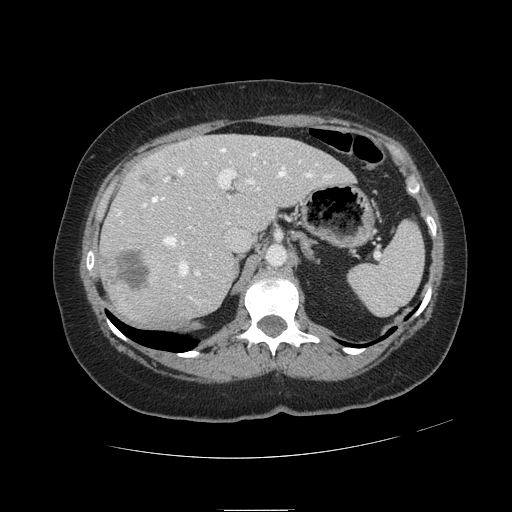
Contrast-enhanced abdominal CT, one axial slice. Position 73 of 121 along the scan axis. Intravenous contrast given. Soft-tissue window (W 400 / L 40 HU). 2.5 mm slice thickness. 512 × 512 image matrix, field of view 400 × 400 mm. Female patient, age 52 years. Case-level facts recorded for this patient, not image findings: diagnosis: colorectal cancer liver metastases, imaged before liver resection; multiple liver metastases: yes; largest metastasis: 6.3 cm; disease in both lobes: no.
Outlined on this slice (manually delineated by an expert):
- hepatic veins: box from (x=118, y=149) to (x=331, y=299) px
- liver: (x=101, y=135)–(x=353, y=323)
- planned liver remnant (the part of the liver to remain after resection): (x=167, y=135)–(x=352, y=230)
- portal vein (with intrahepatic branches): (x=121, y=162)–(x=266, y=276)
- liver metastasis: (x=141, y=169)–(x=156, y=186)
- liver metastasis: (x=118, y=252)–(x=150, y=290)